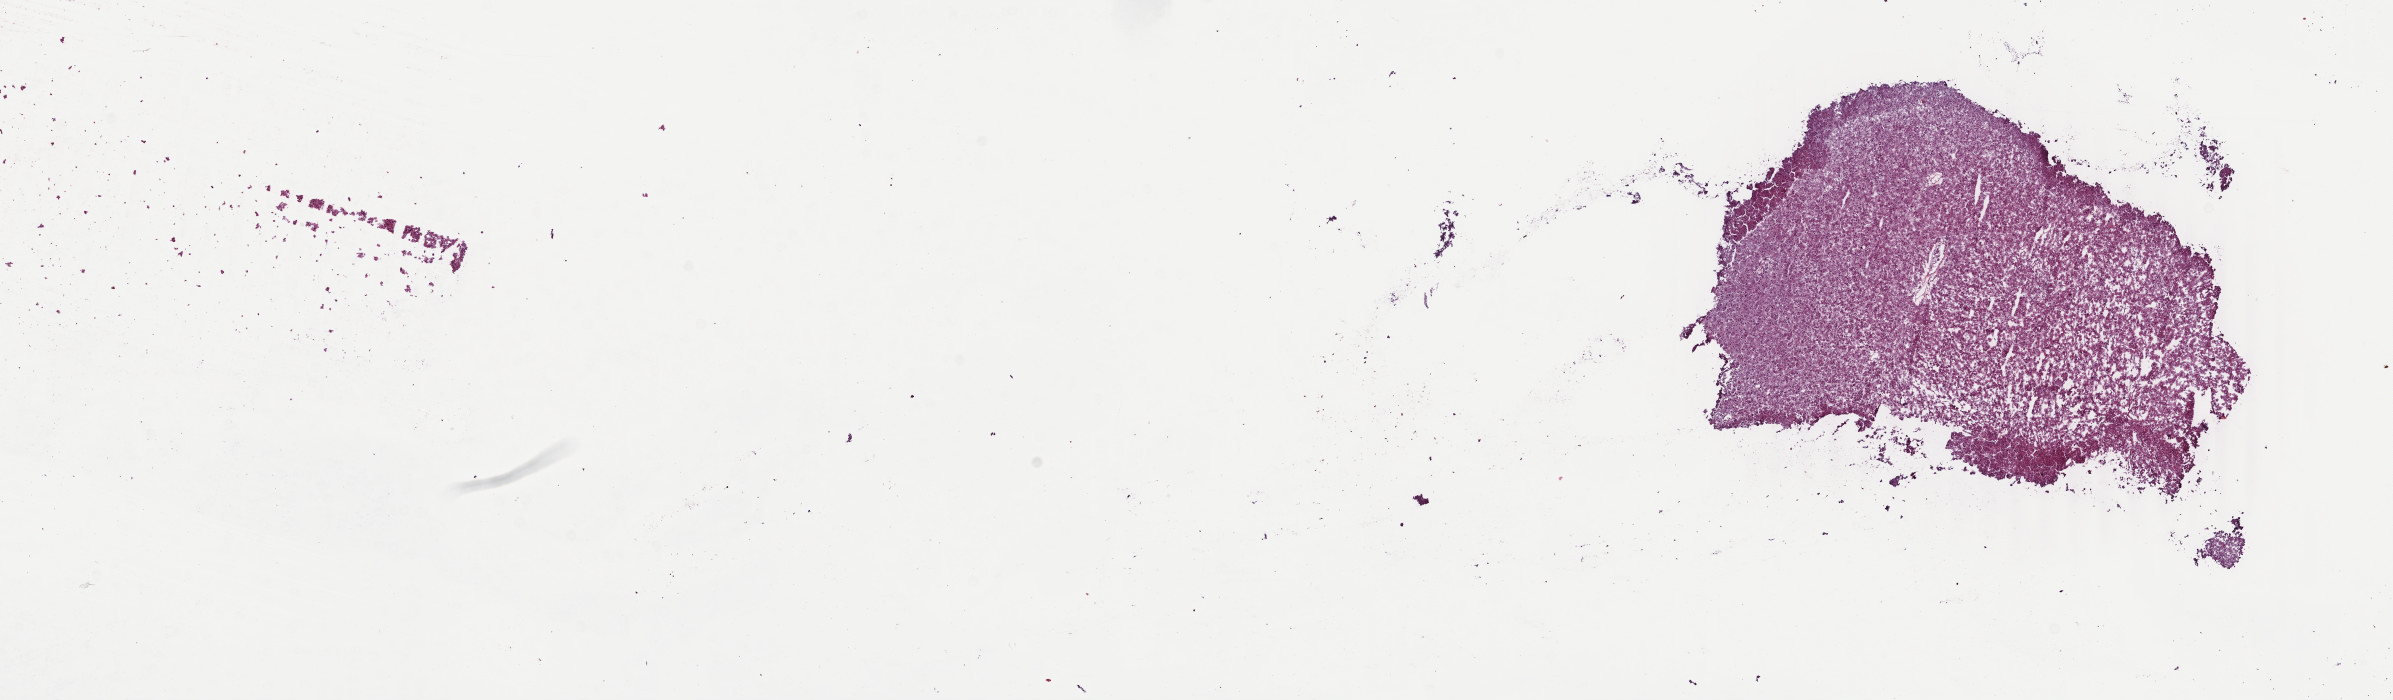
Digitized Hematoxylin and eosin (H&E) stained tissue section (whole slide) — low-resolution overview of the scanned area, about 19.0 x 5.6 mm (slide scanned at 40x), frozen section from the top of the tissue portion, sample: primary tumour, adrenal cortex. Male patient; age at initial diagnosis 51 years. Pathologist review of this section (percent, as recorded): tumour cells 90%, tumour nuclei 90%, normal cells 0%, stromal cells 10%, necrosis 0%. Infiltration values recorded for this section: lymphocyte infiltration 0%, monocyte infiltration 0%, neutrophil infiltration 0%.
Diagnosis: Adrenal cortical carcinoma (cortex of adrenal gland).